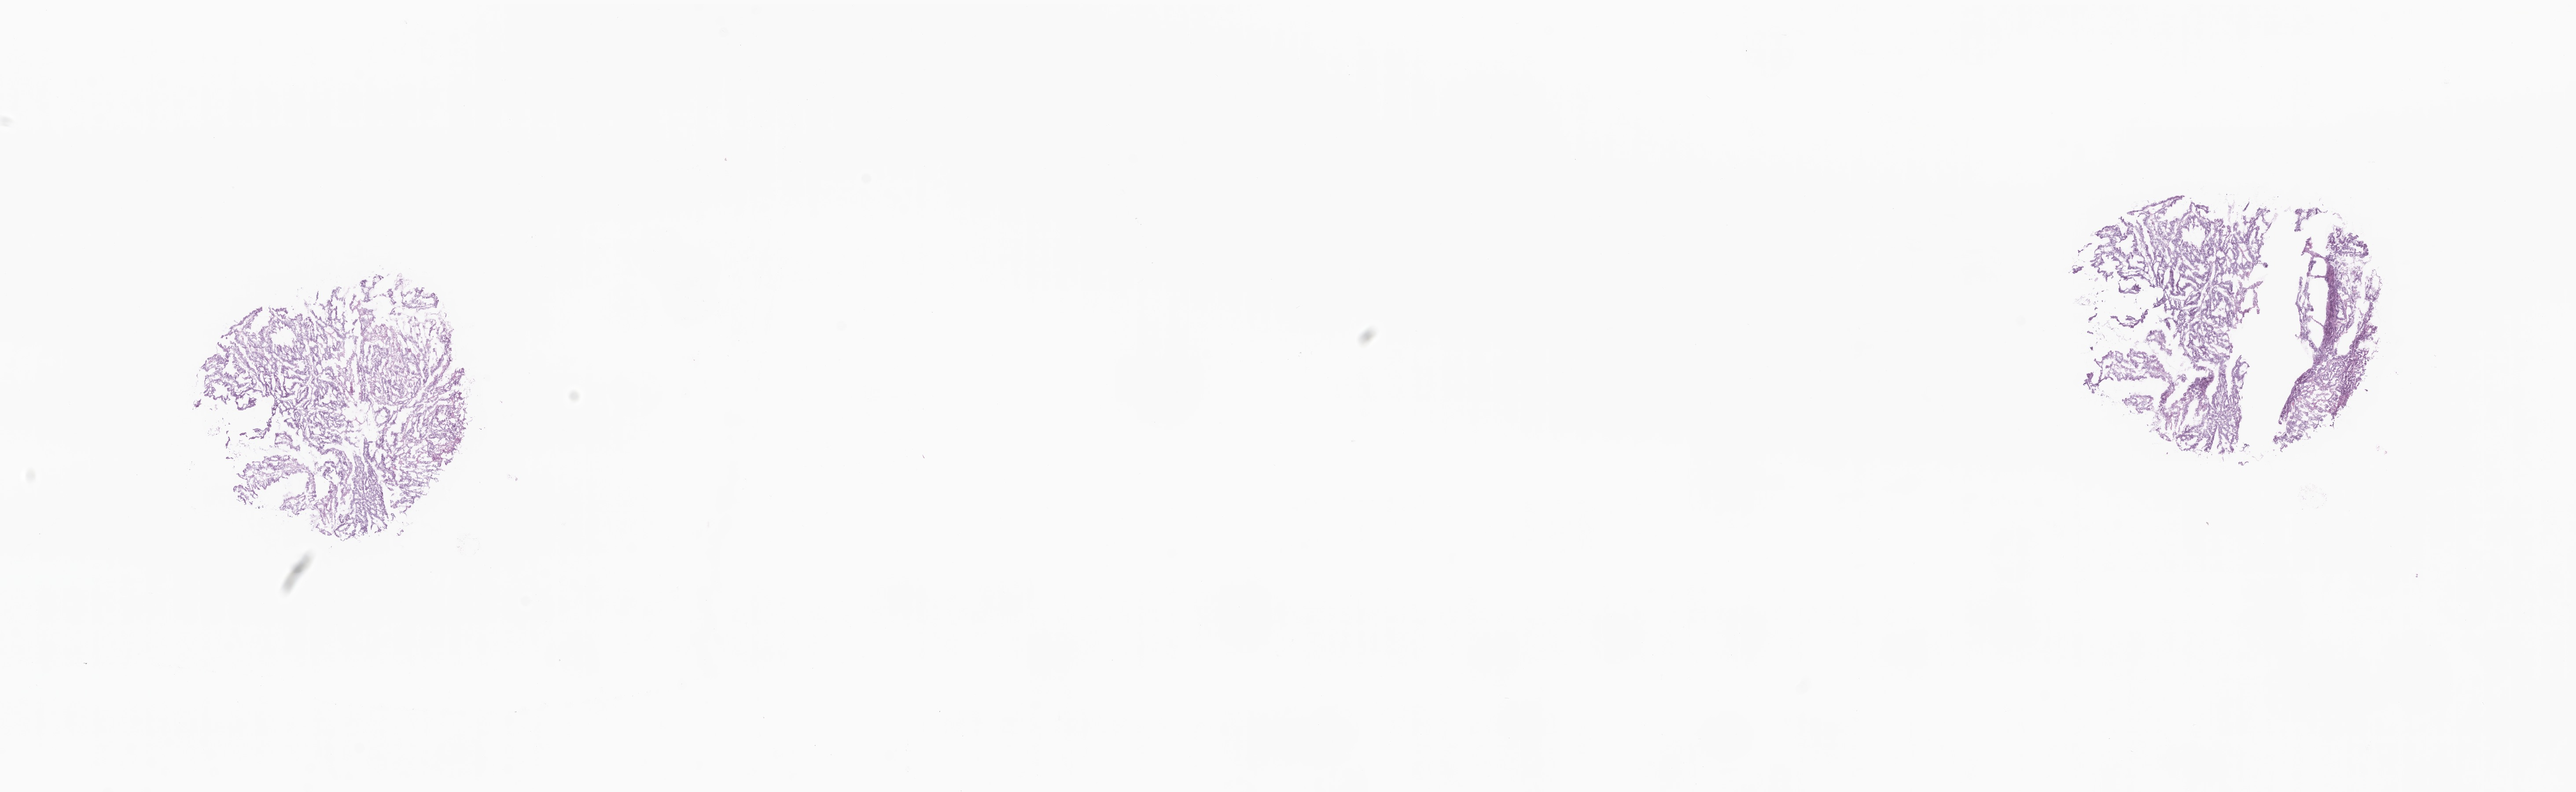
Whole-slide image, H&E stain — whole scanned area (about 24.7 x 7.6 mm) shown as a low-resolution overview, frozen section (tissue freezing medium), specimen: primary tumor, site: ascending colon. Patient: female. Slide review estimates, as recorded: tumor cells 88%, tumor nuclei 95%, stromal cells 11%, necrosis 1%, normal cells 0%. Inflammatory infiltration, as recorded: lymphocyte infiltration 2%, monocyte infiltration 1%, neutrophil infiltration 0%.
Diagnosis: Adenocarcinoma, NOS.